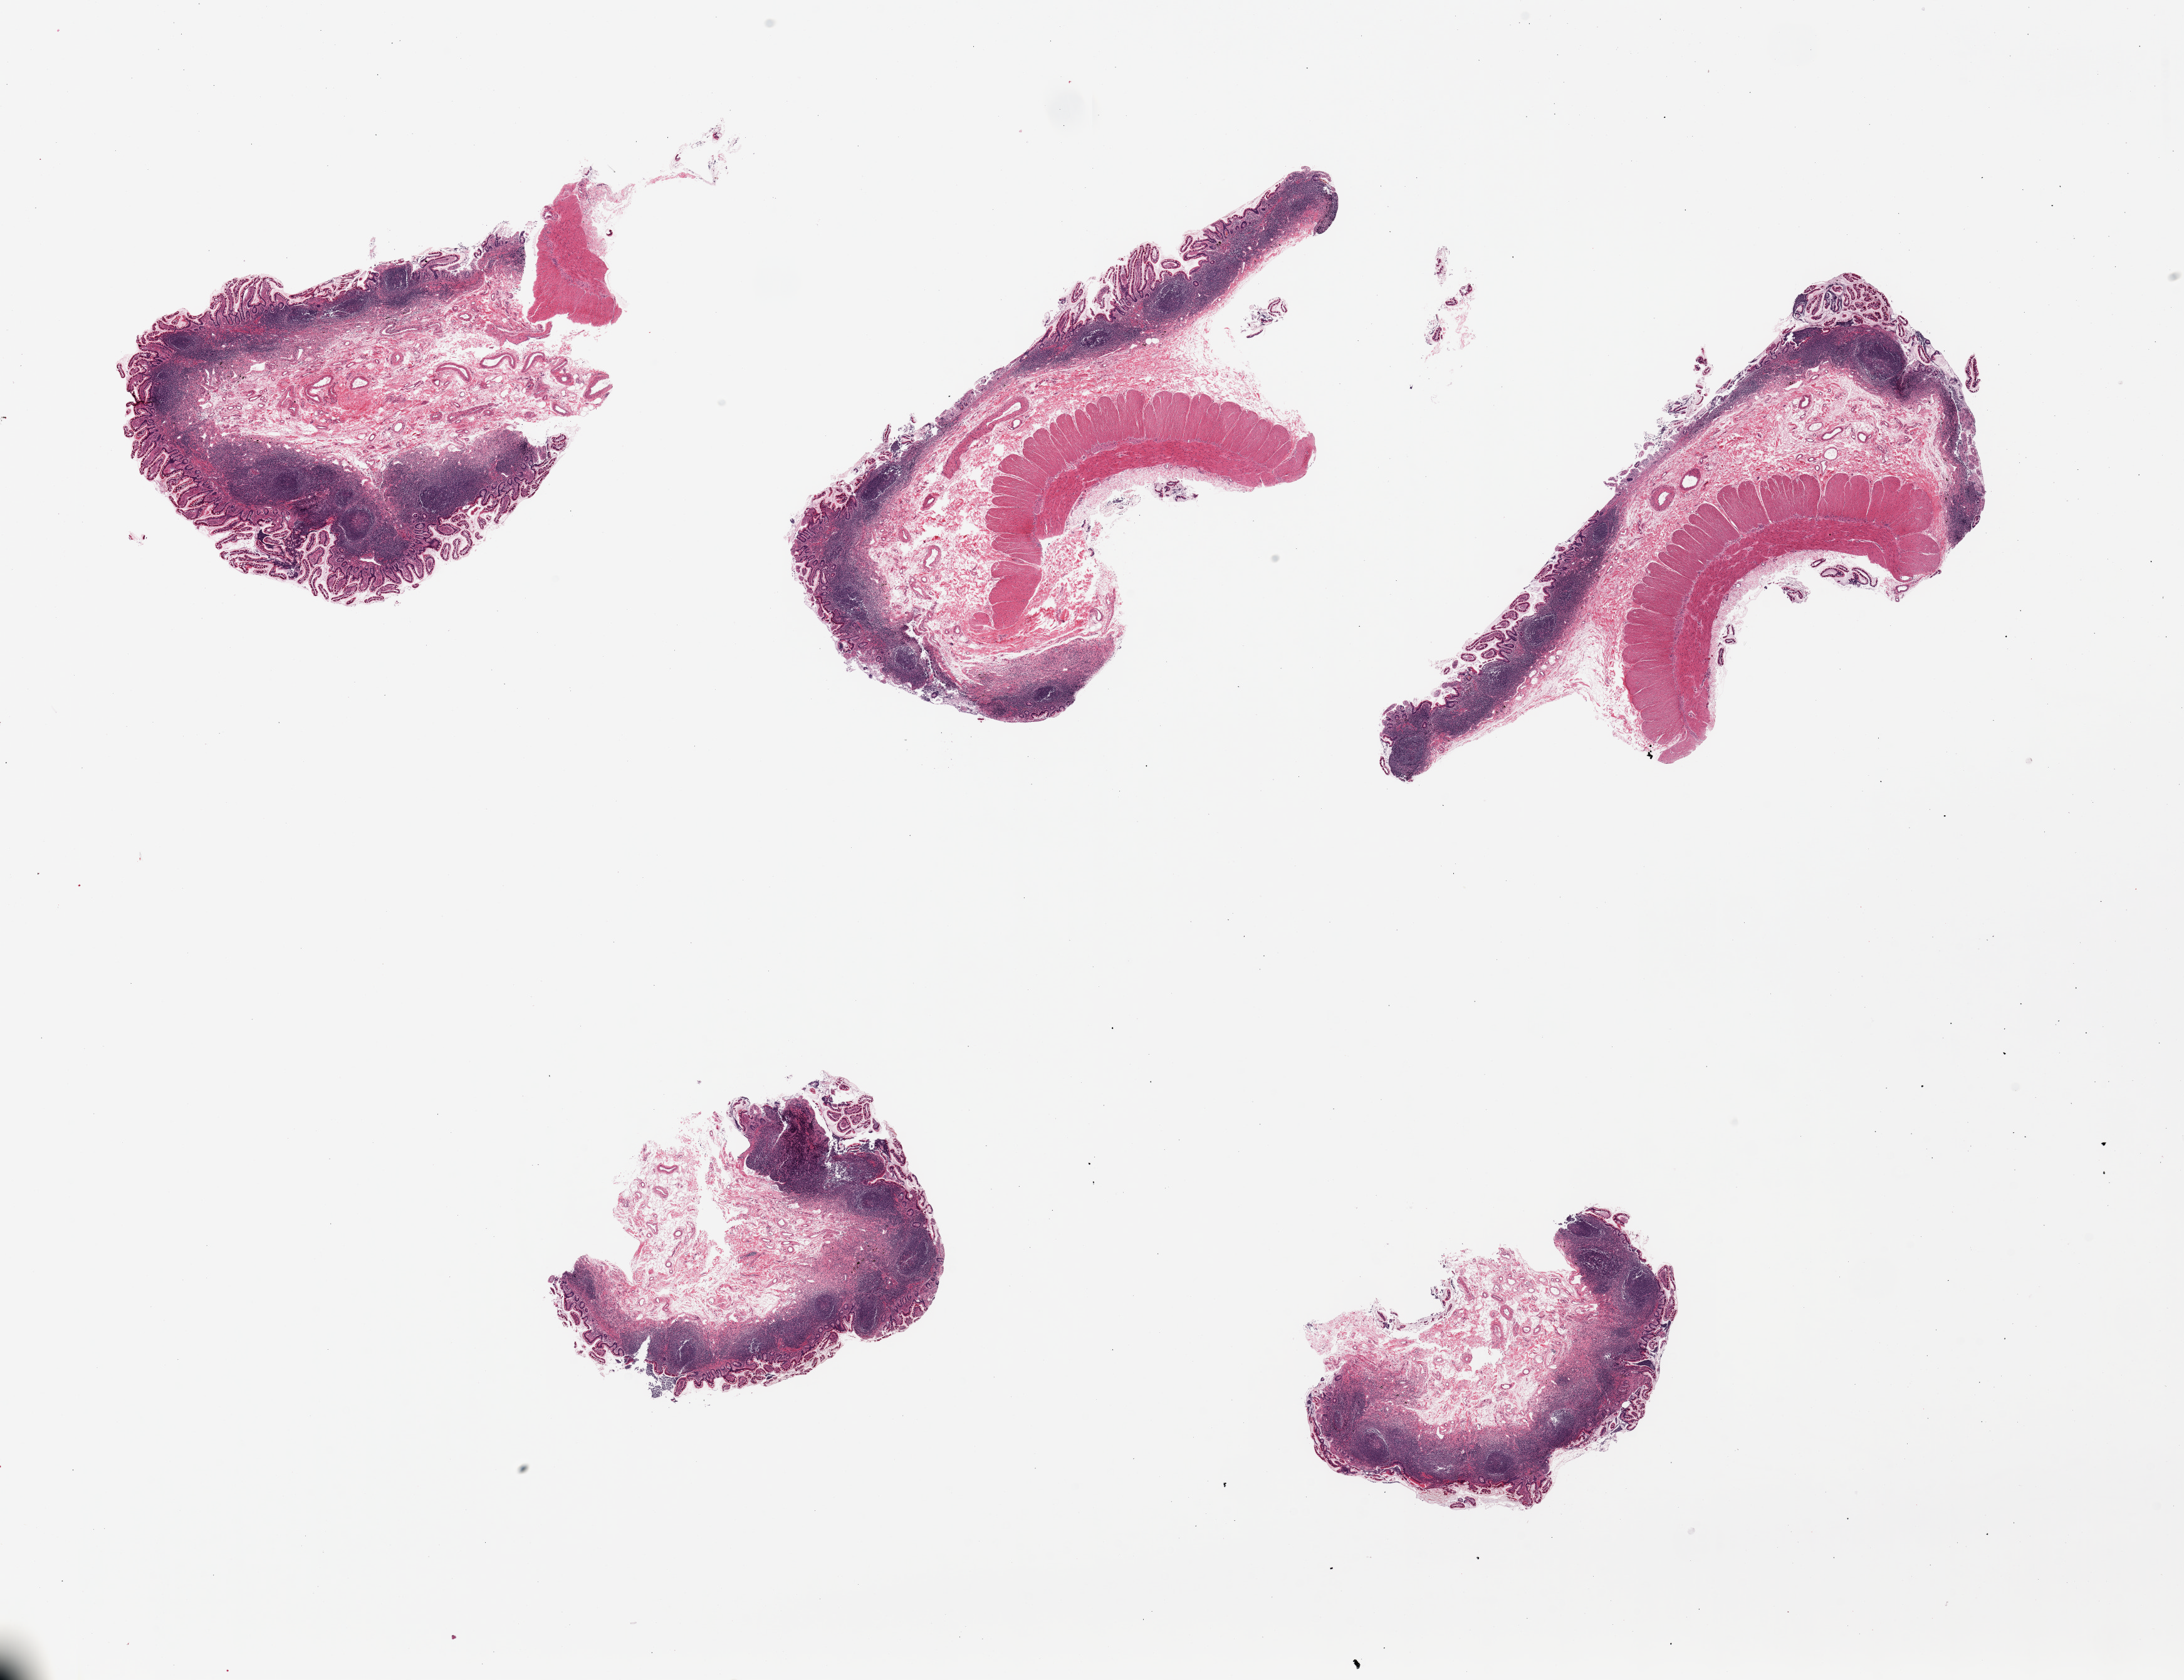
Whole-slide image, hematoxylin and eosin (H&E) stain, whole scanned area (about 27.6 x 21.2 mm) shown as a low-resolution overview. PAXgene-fixed, paraffin-embedded tissue. Target tissue: ileum. Donor tissue sample. Male donor.
• pathologist's review note for this sample: 5 pieces, lymphoid aggregates well-sampled, ~20-25% total